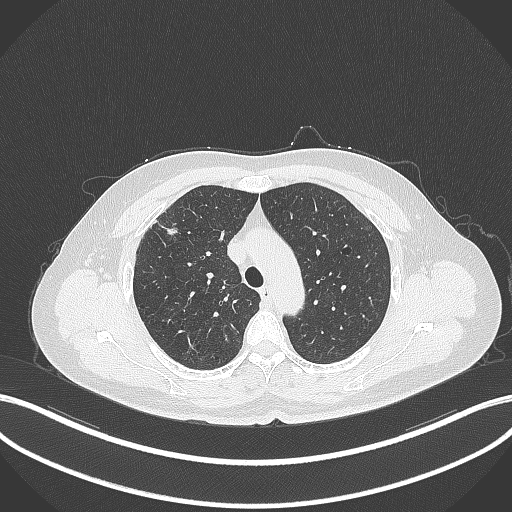
Chest CT, one axial slice; position 271 of 353 along the scan axis; lung window (W 1500 / L -600 HU); 512 × 512 image matrix, field of view 400 × 400 mm. Patient: female, 56 years. Case-level facts recorded for this patient, not image findings: clinical TNM (as recorded): T1c N0 M0.
Annotated regions visible in this slice (rectangle marked by the reading radiologist):
- lung tumour (recorded histology: adenocarcinoma): bounding box [x1, y1, x2, y2] px = [161, 222, 182, 240]